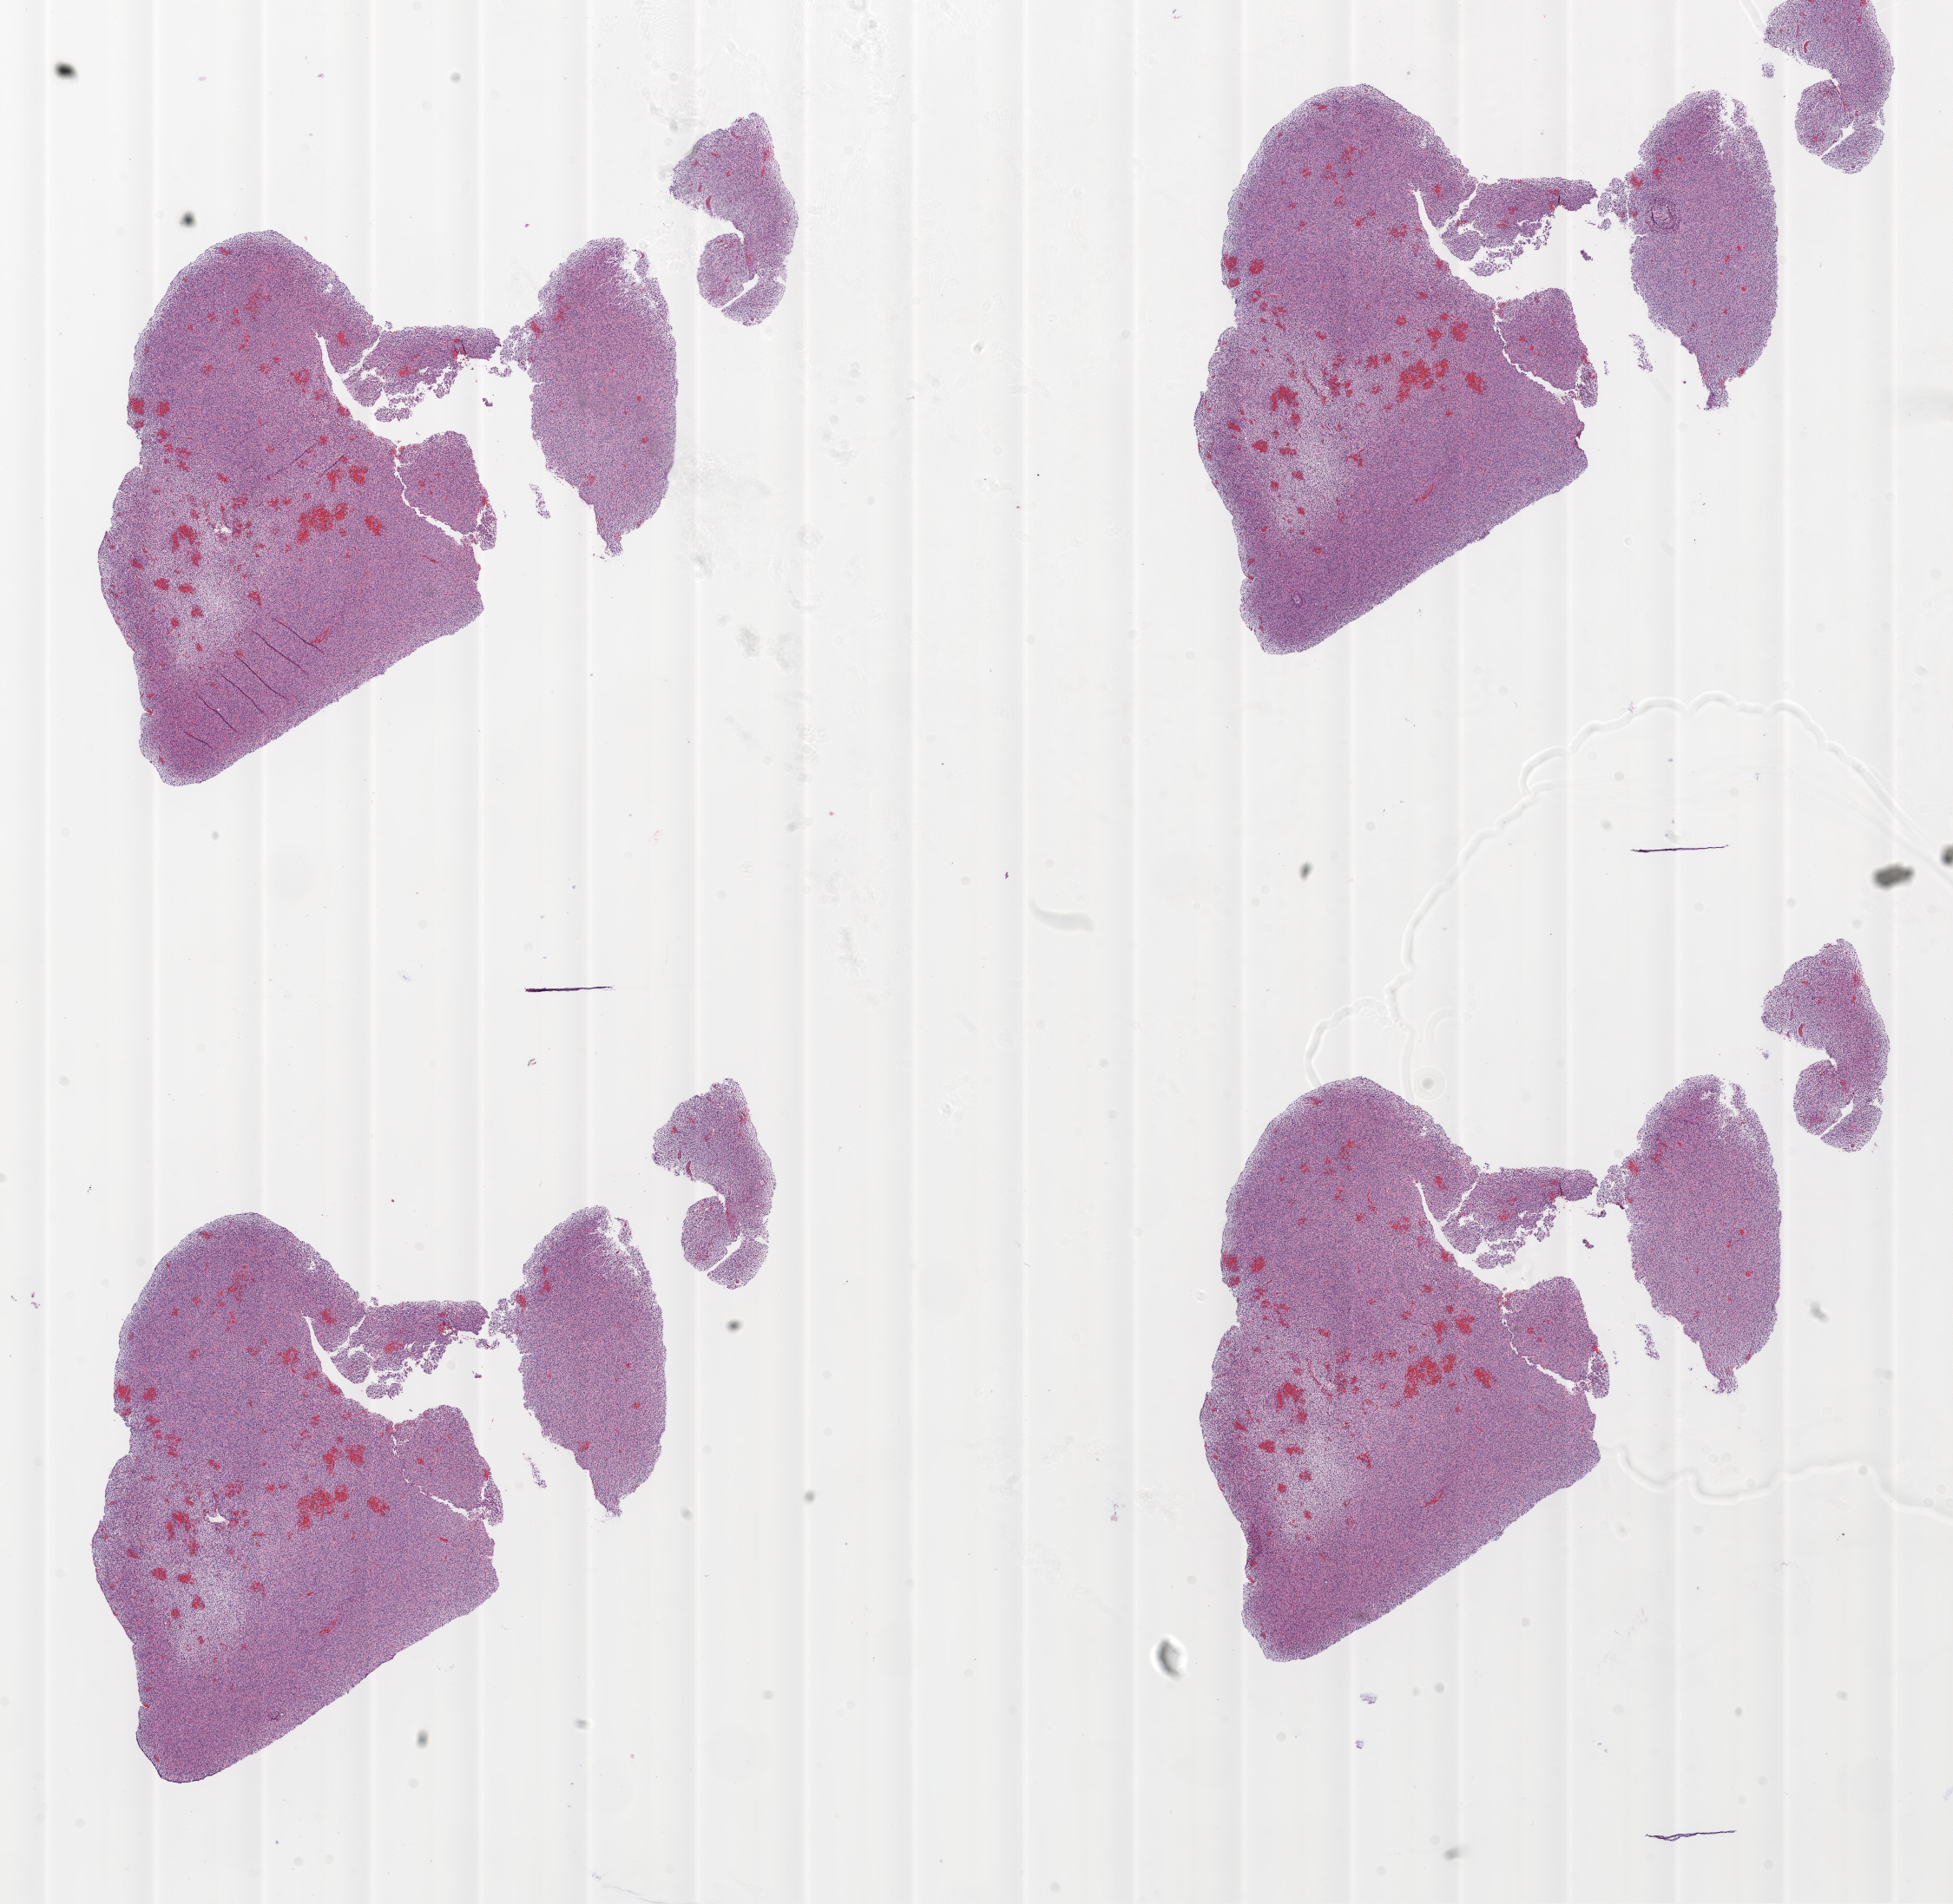
Whole-slide histology image, Hematoxylin and eosin (H&E) stained, whole scanned area (about 18.1 x 17.6 mm) shown as a low-resolution overview. Formalin-fixed paraffin-embedded (FFPE) diagnostic section. Brain, primary tumour sample. Patient: male, age at initial diagnosis 74 years.
Histologic diagnosis: Glioblastoma.